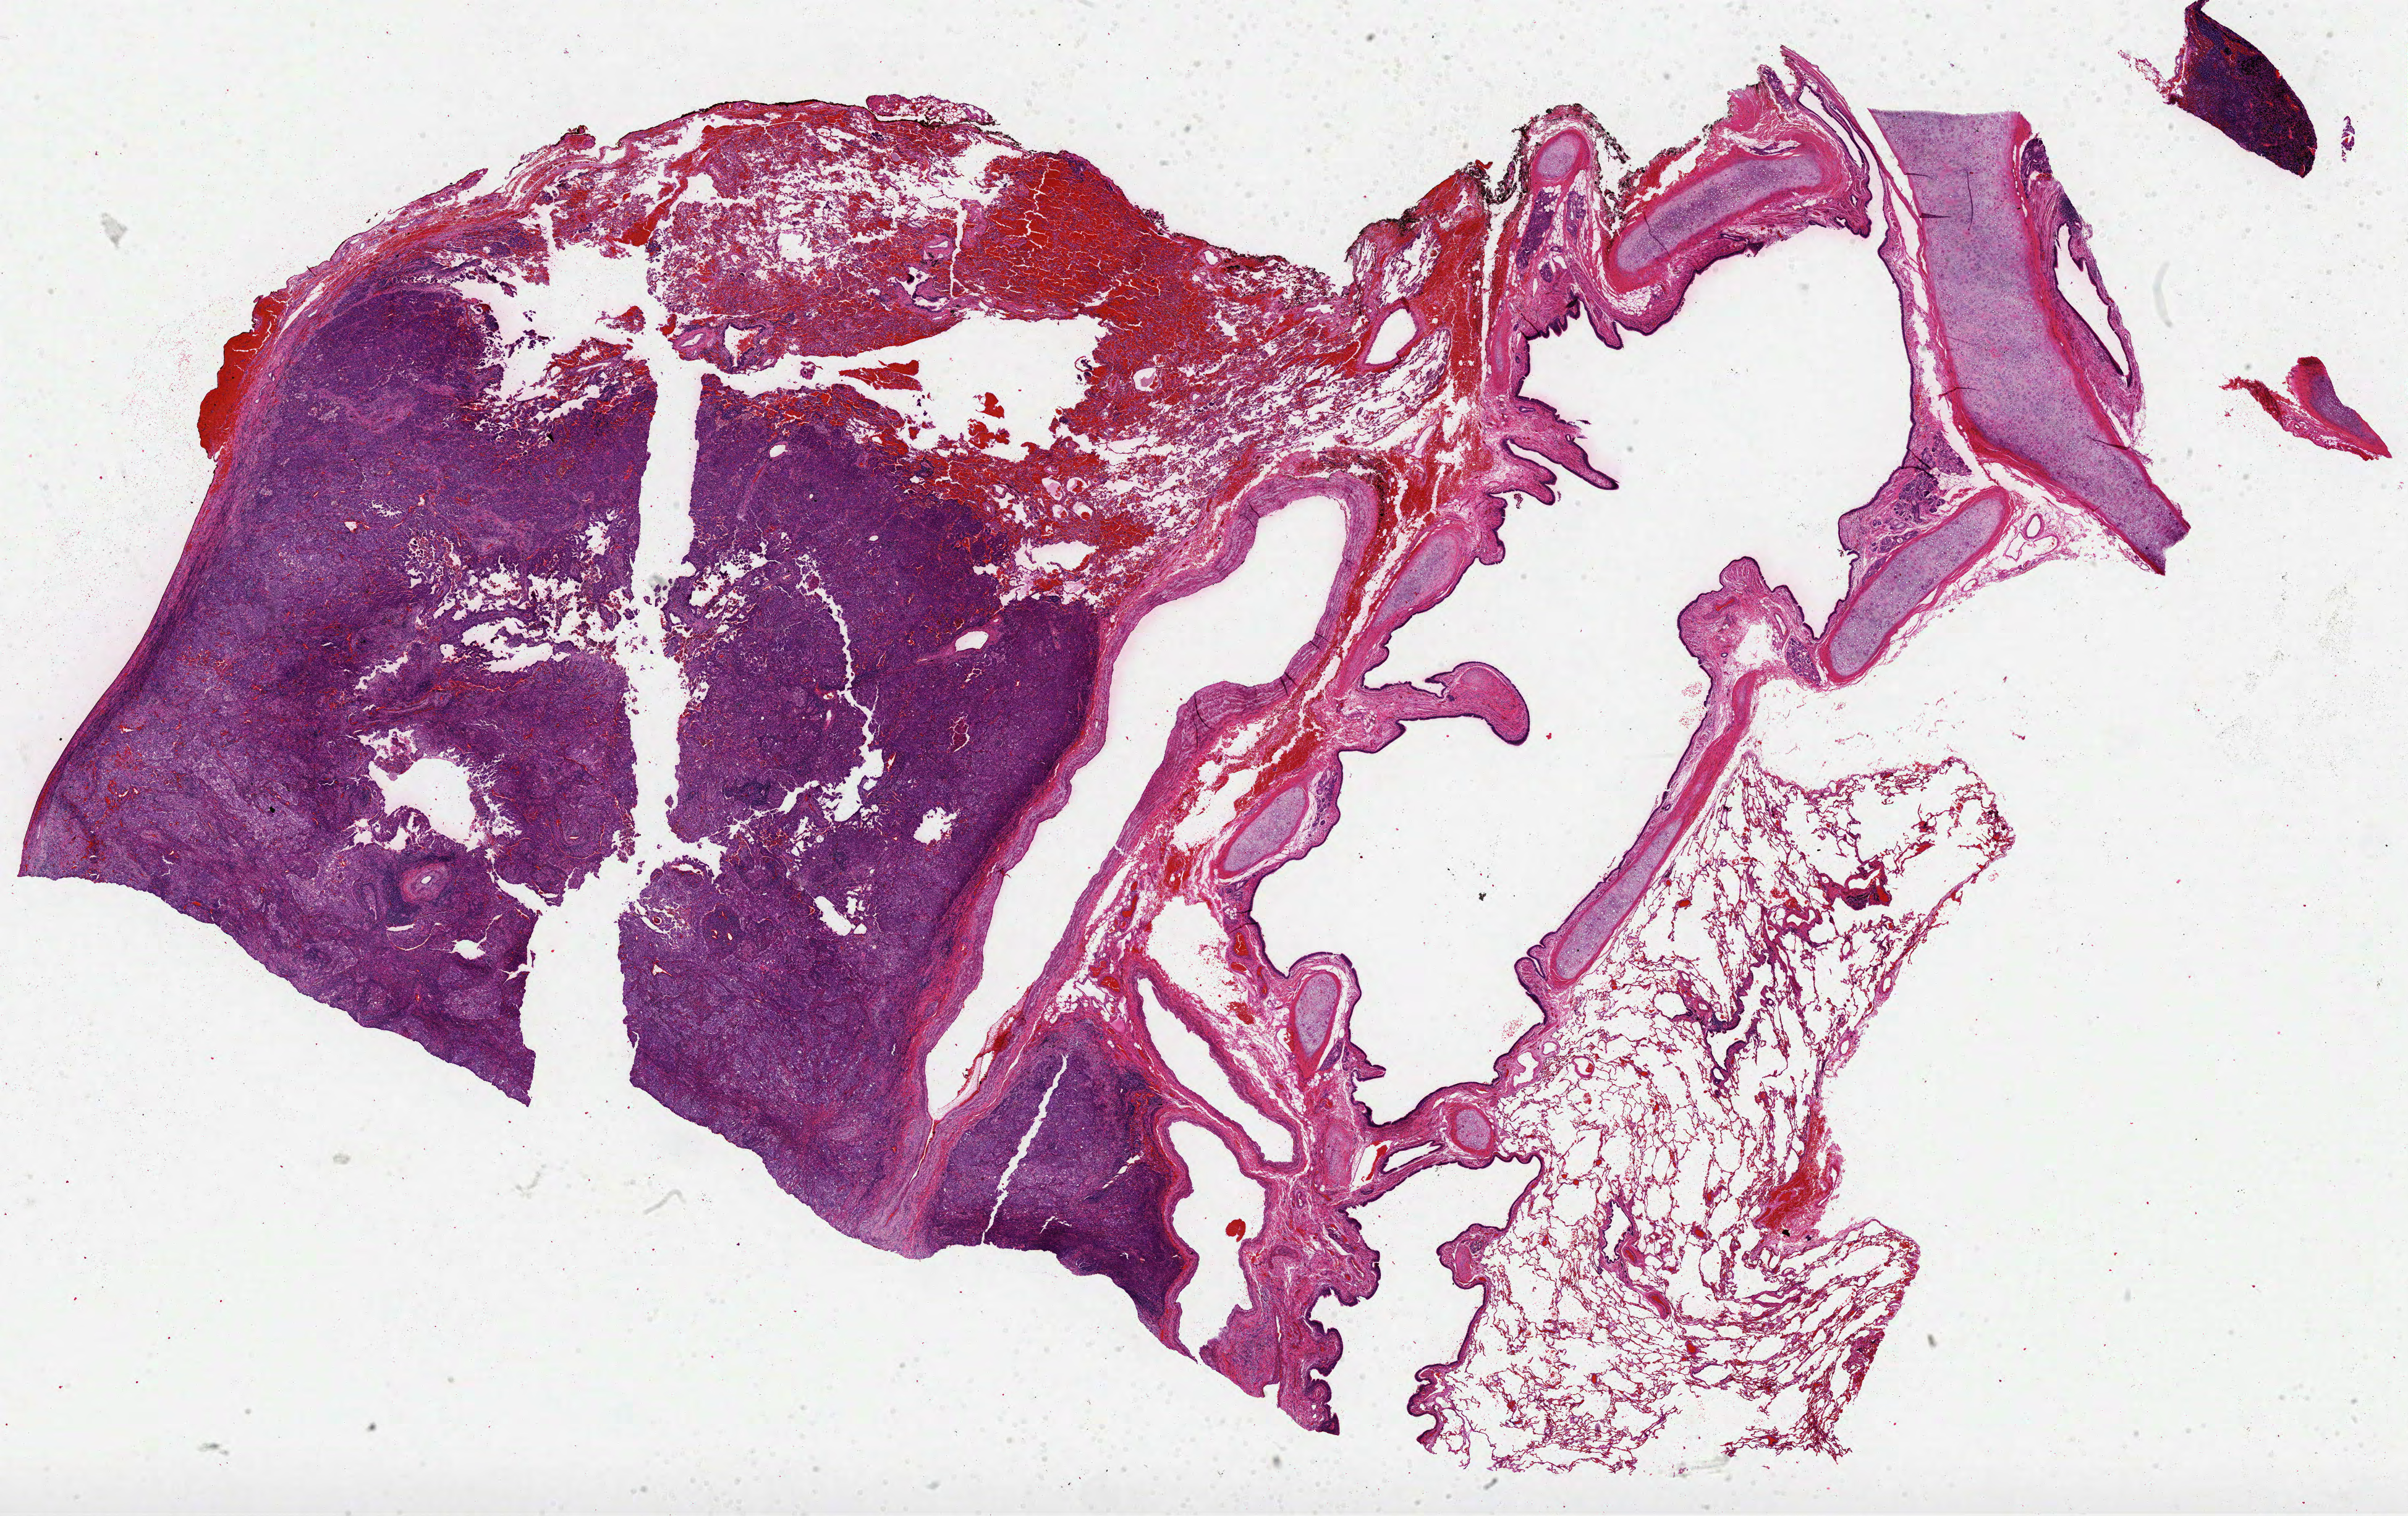
Whole-slide histology image, H&E, a low-resolution overview of the entire scanned area, about 31.4 x 19.8 mm (slide scanned at 40x); FFPE section; sample: primary tumour, lung. Male, age 82 years at initial diagnosis.
Diagnosis: Papillary adenocarcinoma, NOS (upper lobe, lung). AJCC pathologic stage: IIIA (7th edition).